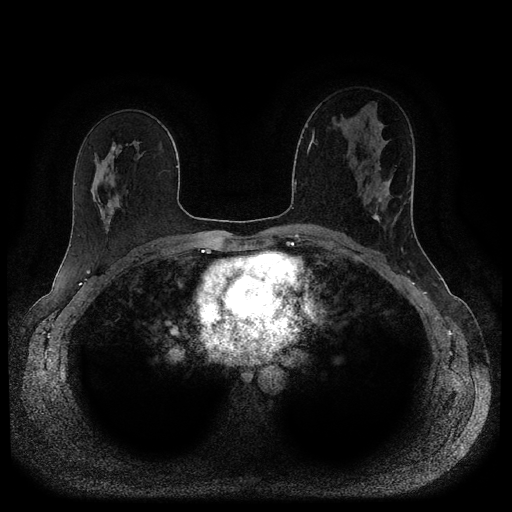
Breast MRI (dynamic contrast-enhanced, multi-phase), one axial slice; slice 57 of 116 in the series (ordered by position); dynamic contrast-enhanced series, time point 2 of 5 at this slice position (early post-contrast); 1.5 T; TE 2.6 ms, TR 5.3 ms; 2 mm slice thickness; 512 × 512 image matrix, field of view 350 × 350 mm. Female patient, age 45 years.
Annotated regions visible in this slice (semi-automatically segmented with operator editing):
- breast lesion (labelled 'tumour' in the annotation; benign lesions carry a separate 'benign' label): bounding box <376,195,382,204> (left, top, right, bottom; pixels)